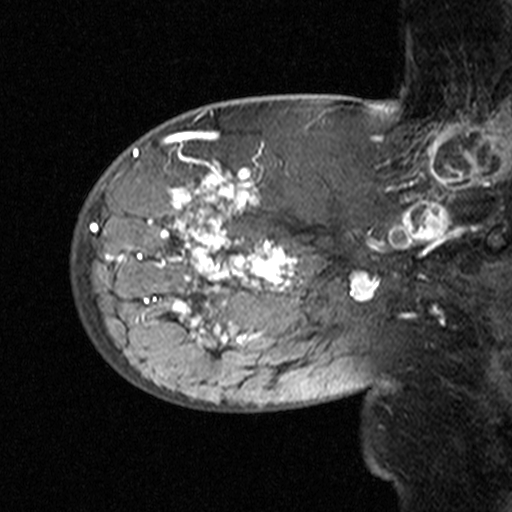
Breast MRI (dynamic contrast-enhanced), one sagittal slice. Slice 14 of 44 in the series (ordered by position). Dynamic contrast-enhanced study with each time point stored as its own series, time point 2 of 3 at this slice position (early post-contrast, ordered by acquisition time). 1.5 T. TE 4.5 ms, TR 11 ms. 3 mm slice thickness. 512 × 512 image matrix, field of view 200 × 200 mm. Female patient, age 53 years. From the clinical record (not read from this slice): setting: breast cancer imaged before/during neoadjuvant chemotherapy; receptor status: HR-positive, HER2-negative.
Annotated regions visible in this slice (semi-automatic segmentation, software-assisted and operator-edited):
- analysis volume of interest (the breast-tissue region the enhancement analysis was run in; not a lesion): bounding box [x1, y1, x2, y2] px = [76, 140, 311, 353]
- tumour enhancement mask (voxels above the 90 % enhancement threshold inside the analysis volume of interest): [117, 161, 297, 347]